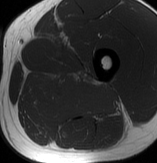
MRI of an extremity soft-tissue mass, one axial slice. Slice 45 of 70 in the series (ordered by position). MR volume resampled by the dataset authors to the PET/CT grid (not the native acquisition matrix). 3.27 mm slice thickness. 157 × 163 image matrix, field of view 153 × 159 mm. Male patient. Case-level facts recorded for this patient, not image findings: histological type: extraskeletal osteosarcoma; grade: high; site of the primary tumour: left adductur.
Annotated regions visible in this slice (expert contour drawn on MRI and transferred to this co-registered scan by the dataset authors):
- gross tumour volume (mass): box from (x=26, y=69) to (x=123, y=123) px